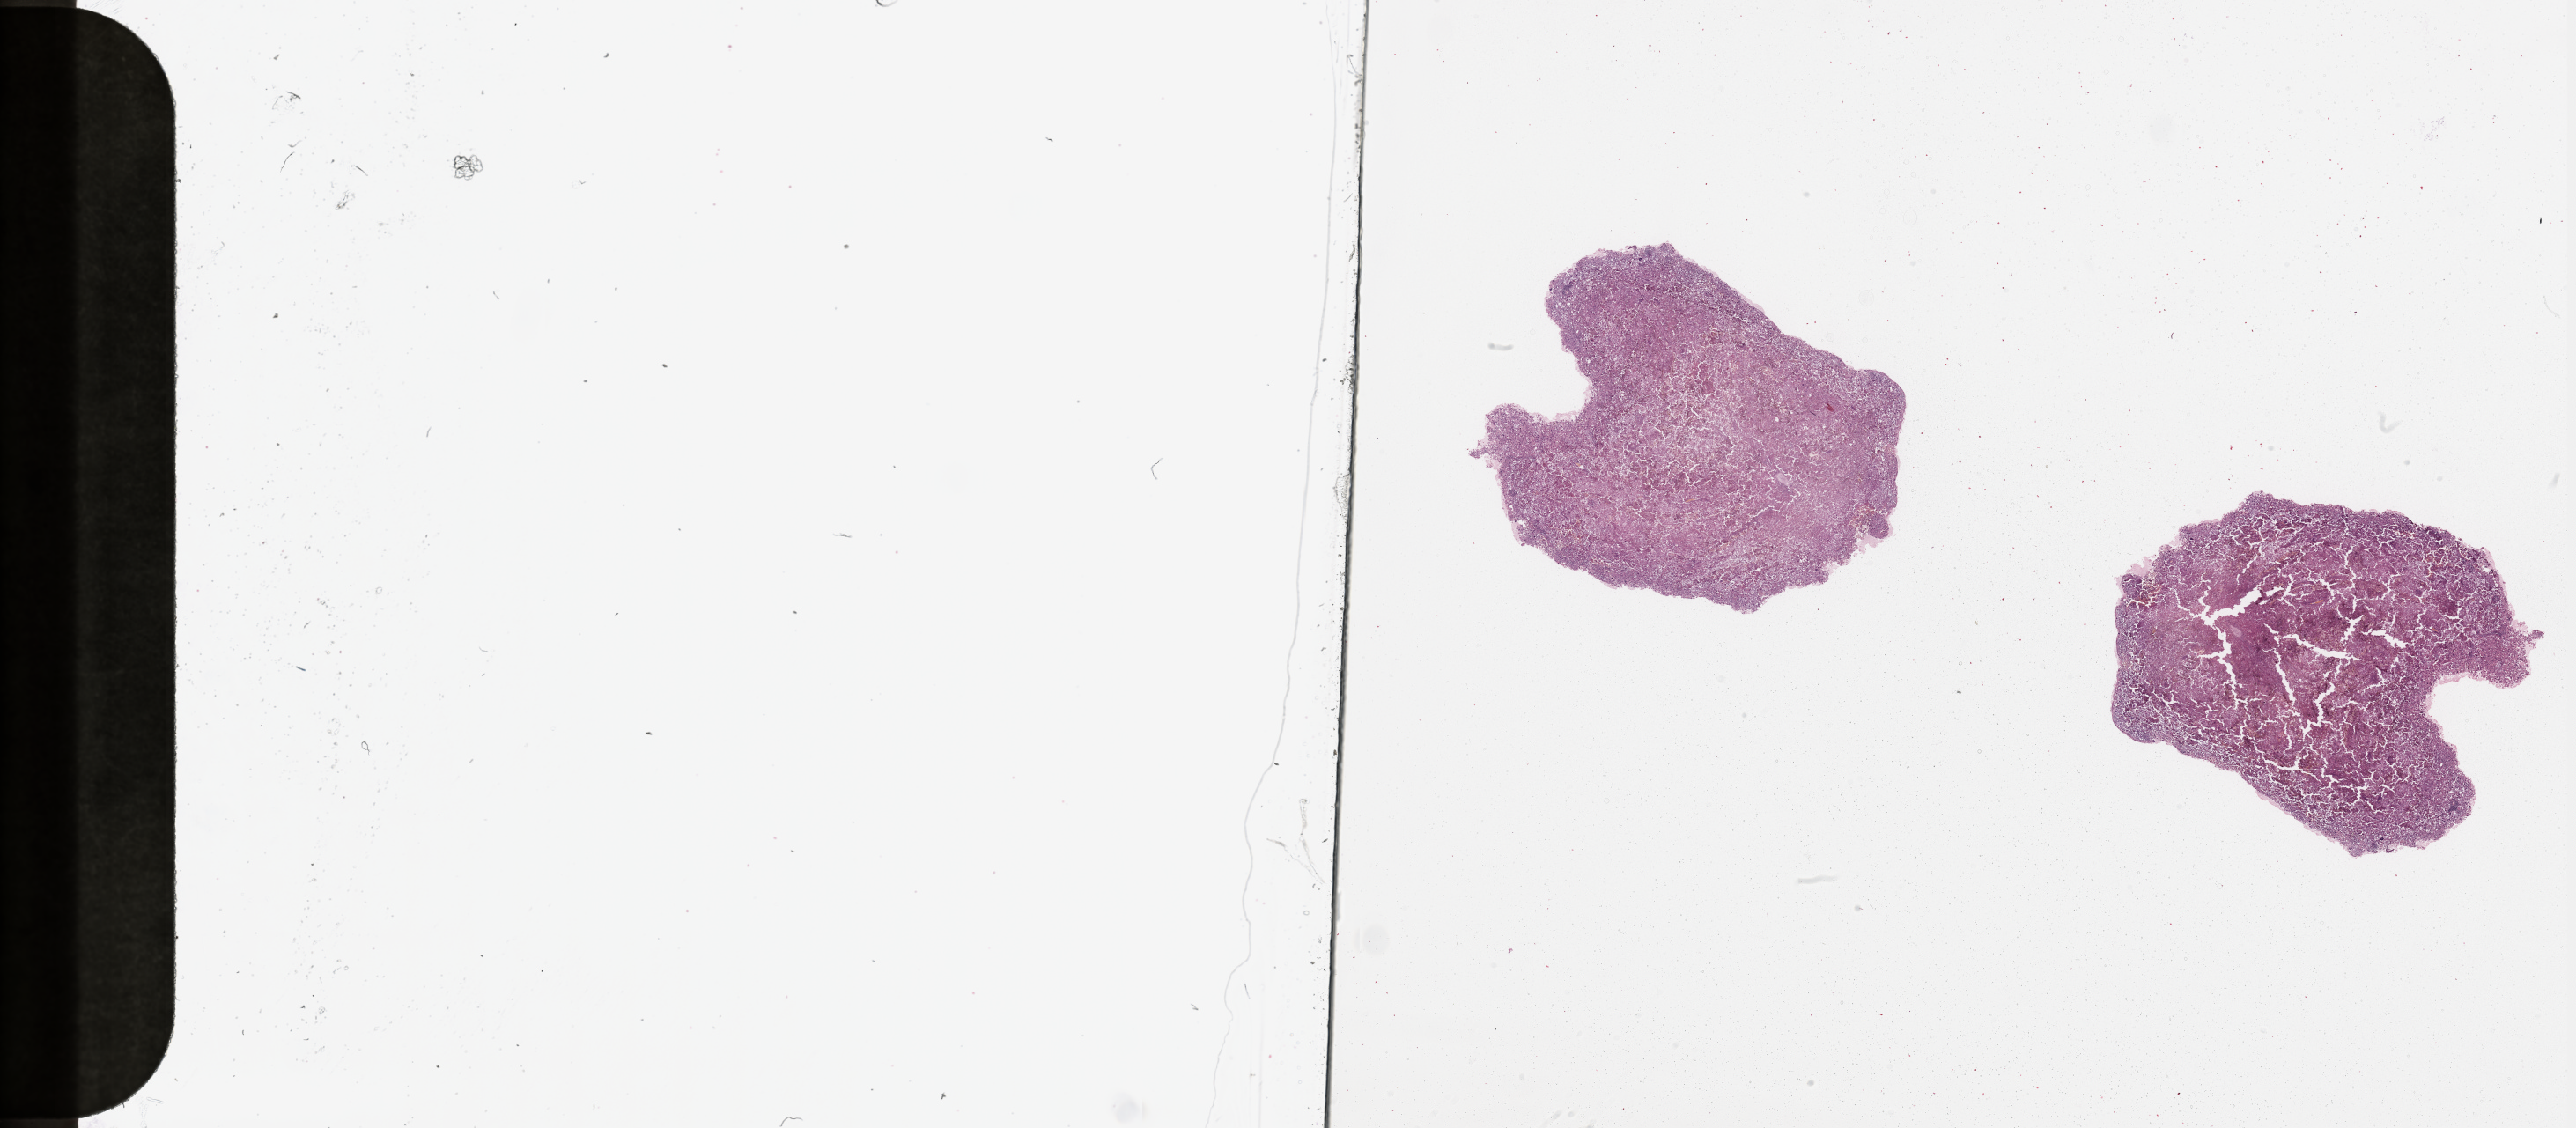
Digitized Hematoxylin and eosin (H&E) stained tissue section (whole slide), whole scanned area (about 46.3 x 20.3 mm, slide scanned at 20x) shown as a low-resolution overview; tumour tissue sample, sampled site: lymph node. Patient: male, age 33 years. Slide review estimates, as recorded: tumour nuclei 95%, necrosis 5%.
This section: metastatic tumour tissue. Patient diagnosis: Malignant melanoma, NOS. Primary tumour site (as recorded): trunk.